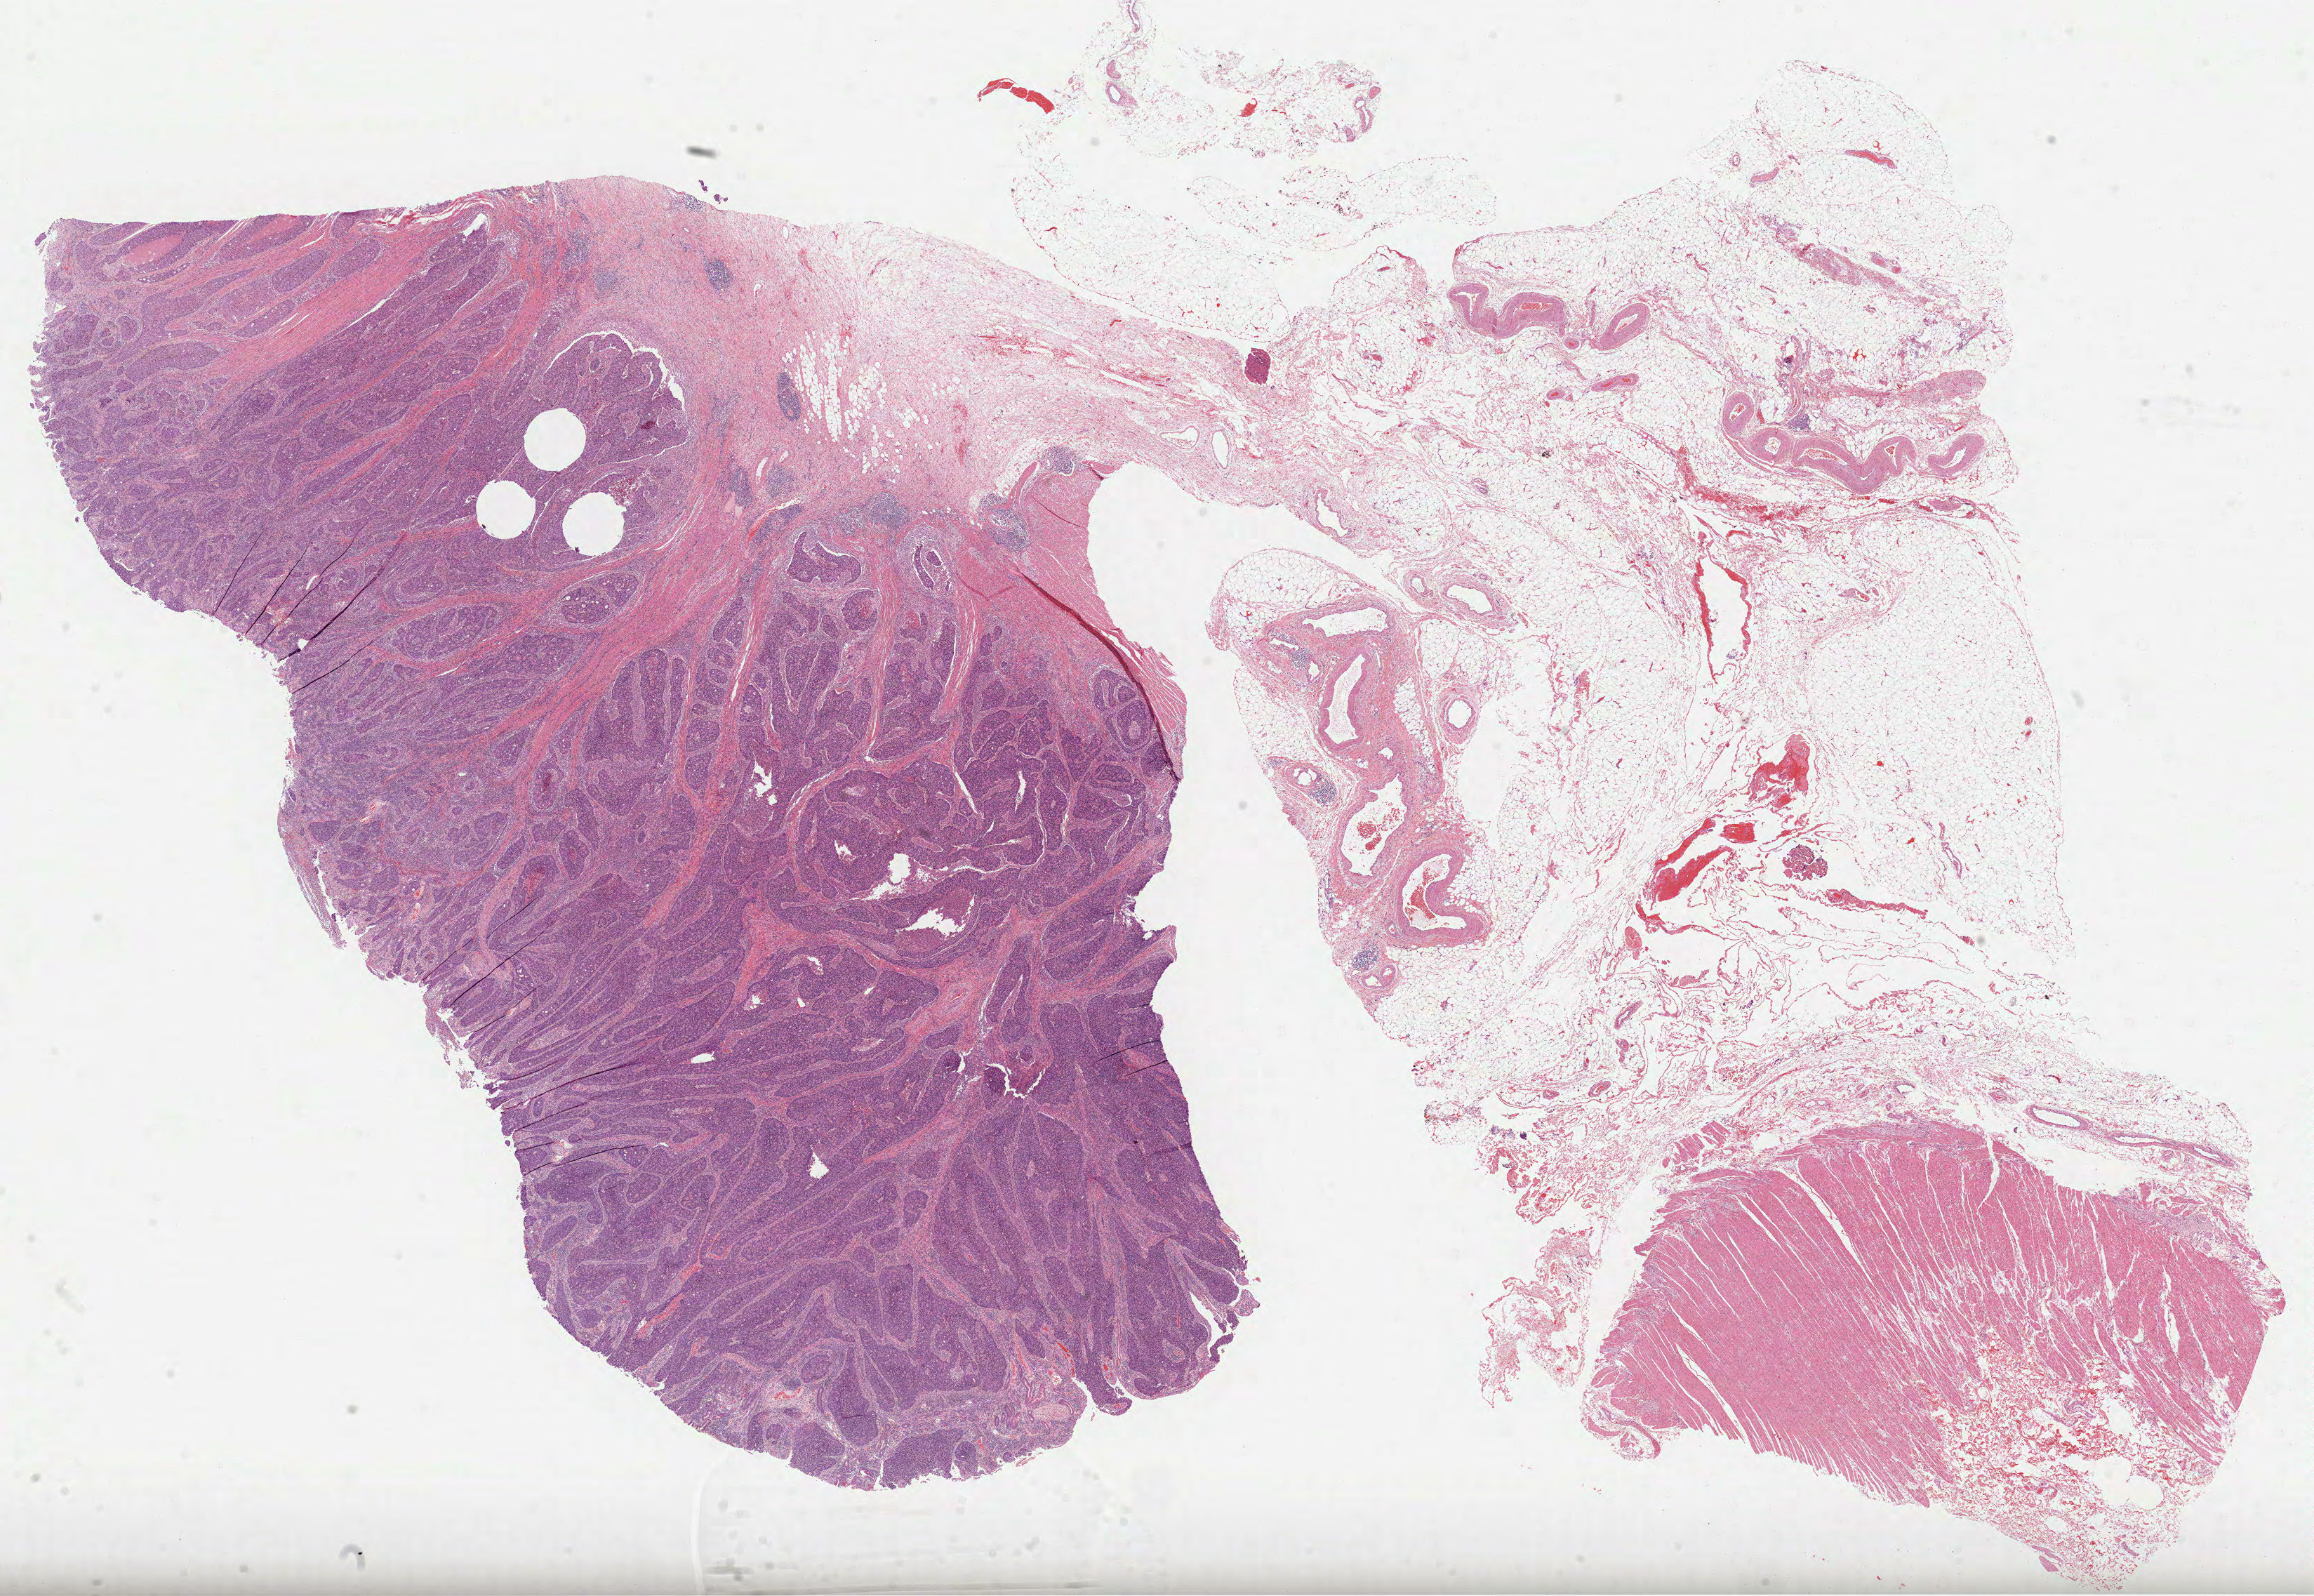
Whole-slide histology image, H&E, whole scanned area (about 26.6 x 18.3 mm, acquisition: 40x scan) shown as a low-resolution overview; formalin-fixed paraffin-embedded (FFPE) diagnostic section; primary tumour sample from the colon. Patient: female, age at initial diagnosis 70 years.
AJCC pathologic stage: II (6th edition). TNM: T3 N0 M0. Histologic diagnosis: Adenocarcinoma, NOS (cecum).